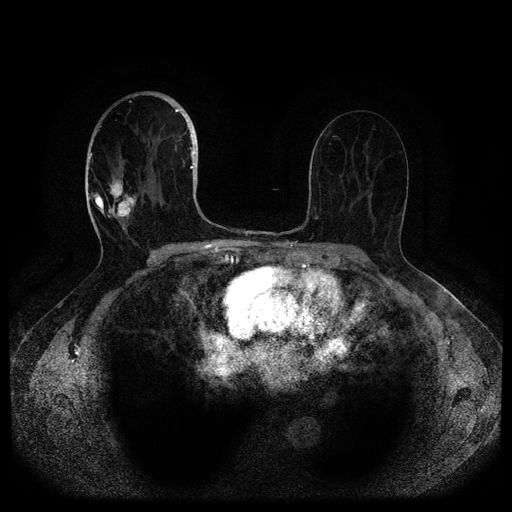
Breast MRI (dynamic contrast-enhanced, multi-phase), one axial slice. Position 56 of 116 along the scan axis. Dynamic contrast-enhanced series, time point 2 of 5 at this slice position (early post-contrast). 1.5 T. TE 2.6 ms, TR 5.3 ms. 2 mm slice thickness. 512 × 512 image matrix, field of view 350 × 350 mm. Female patient, age 82 years.
Outlined on this slice (semi-automatically segmented with operator editing):
- breast lesion (labelled 'tumour' in the annotation; benign lesions carry a separate 'benign' label): box from (x=107, y=177) to (x=137, y=221) px